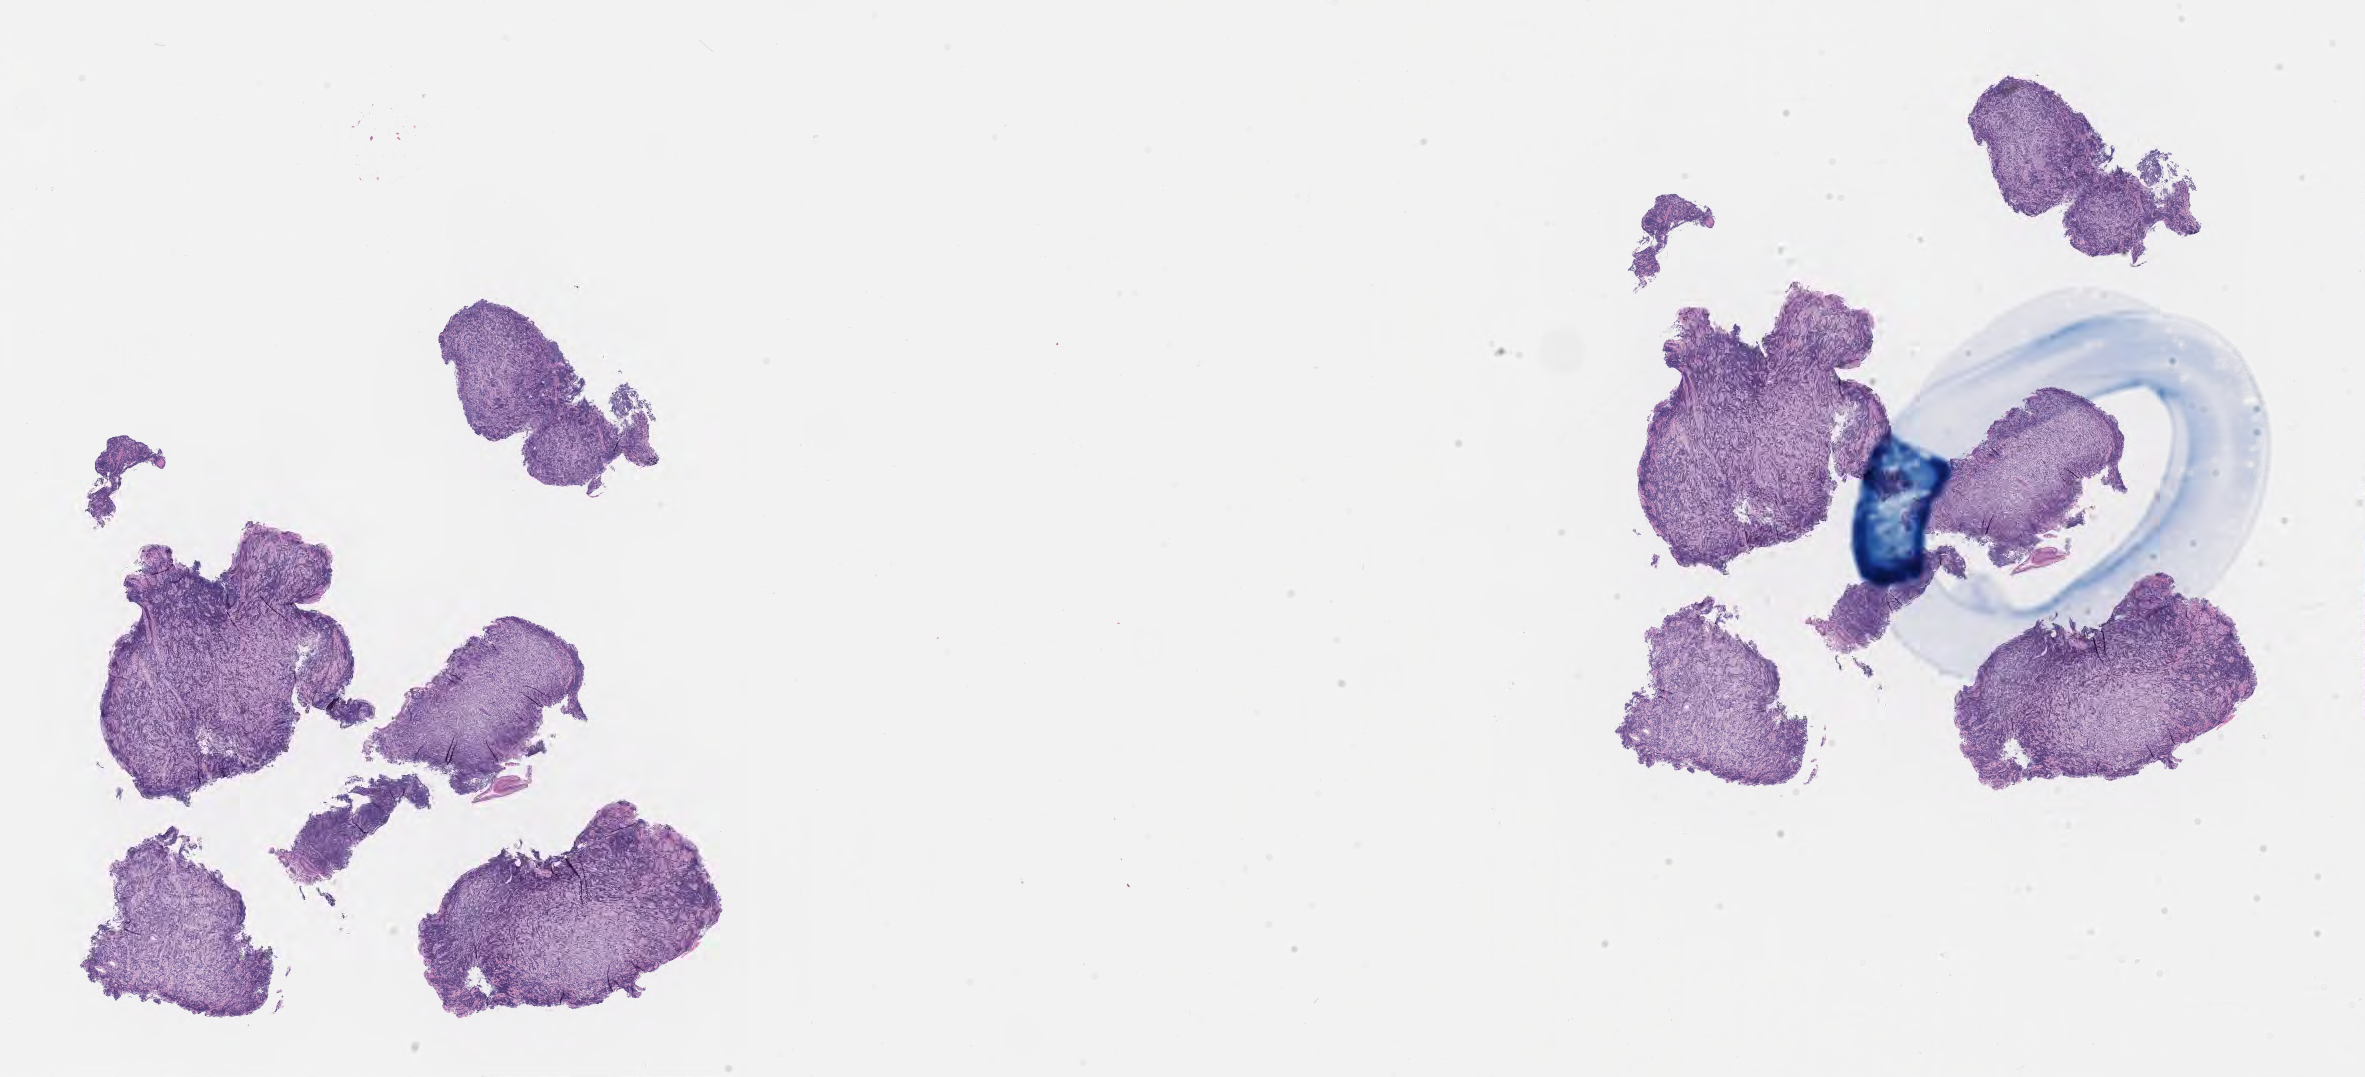
Digitized hematoxylin and eosin (H&E)-stained section, low-resolution overview of the scanned area, about 19.1 x 8.7 mm; specimen: tumor tissue; anatomic site: small intestine. Female patient, age 47 years.
Diagnosis: Burkitt lymphoma, NOS.